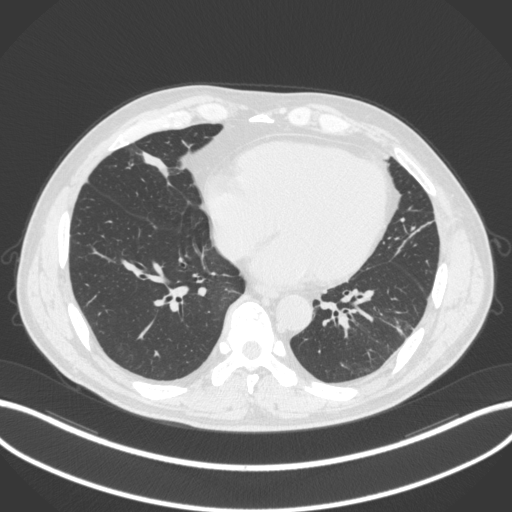
Chest CT, one axial slice. Slice 91 of 399 in the series (ordered by position). Reconstruction kernel B31f. 120 kVp. Lung window (W 1500 / L -600 HU). 1 mm slice thickness. 512 × 512 image matrix. Male patient, age 59 years. From the clinical record (not read from this slice): clinical TNM (as recorded): T2a N1 M0.
Outlined on this slice (rectangle marked by the reading radiologist):
- lung tumour (recorded histology: adenocarcinoma): bounding box [x1, y1, x2, y2] px = [138, 145, 179, 189]